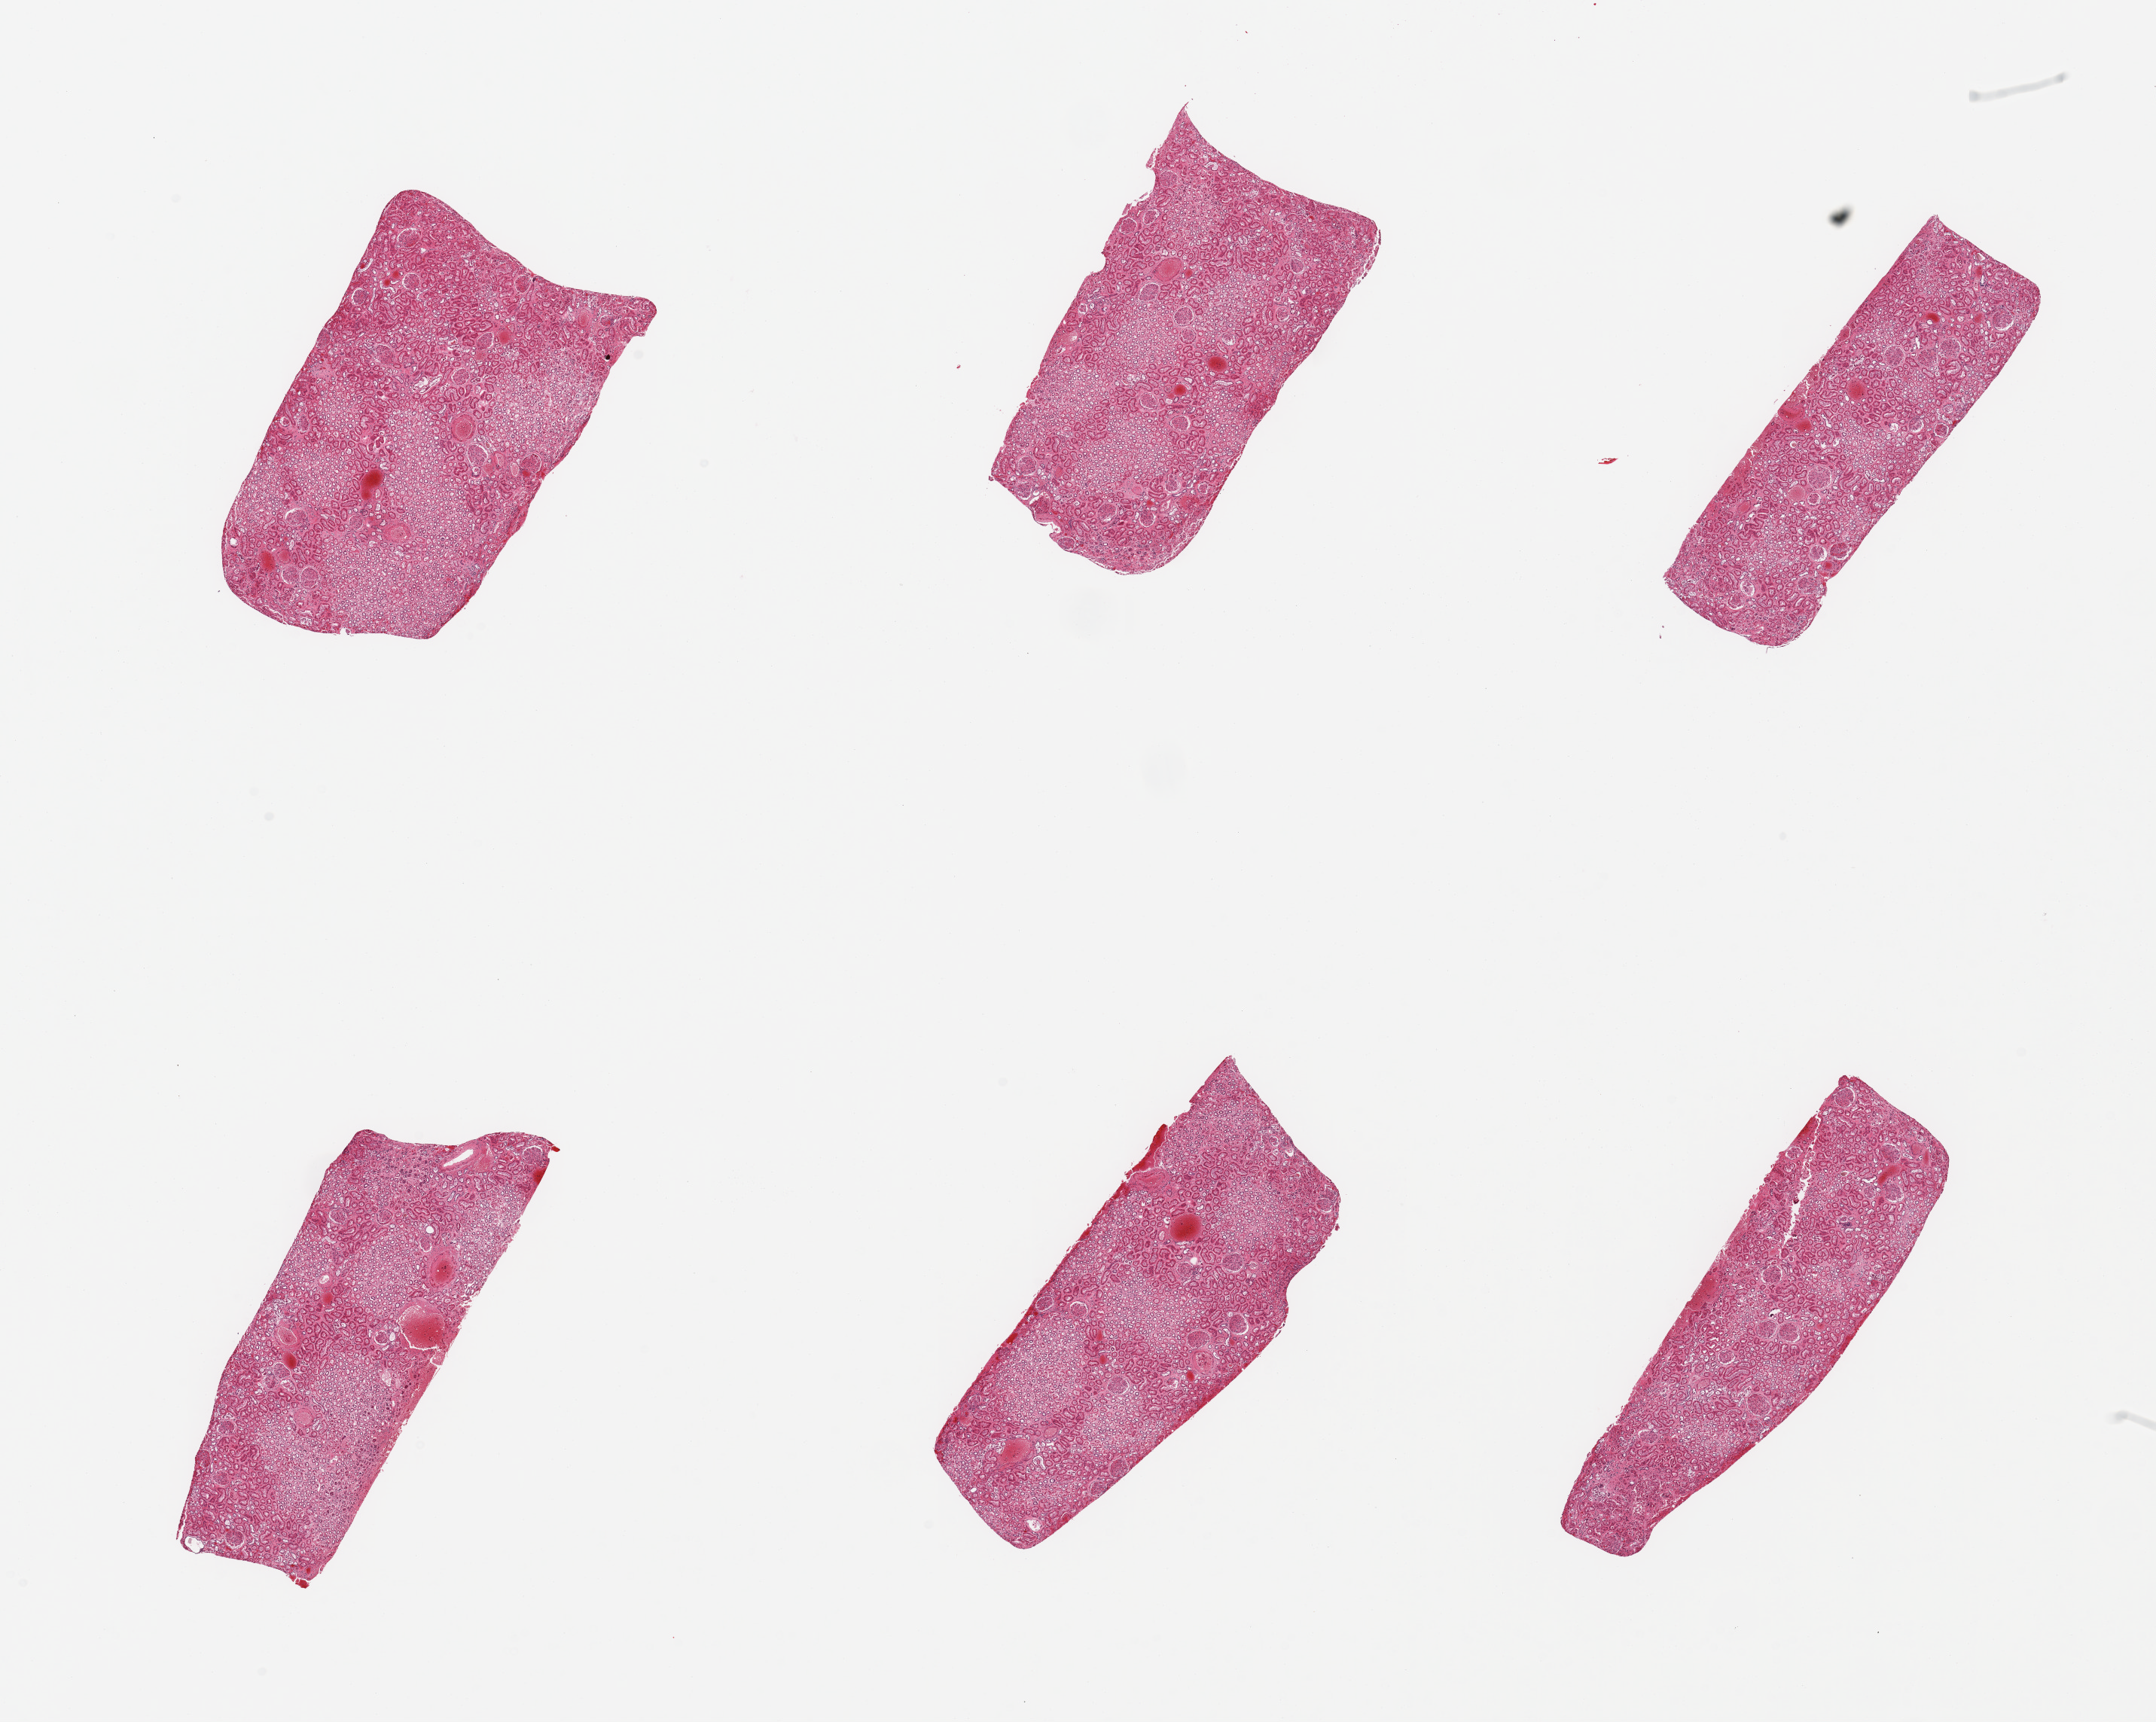
Hematoxylin and eosin (H&E) whole-slide image — low-resolution overview of the scanned area, about 22.6 x 18.1 mm; PAXgene-fixed, paraffin-embedded tissue; target tissue: renal cortex; donor tissue sample. Donor: female.
Pathologist's review note for this sample: 6 pieces; congested, arterio/arteriolosclerosis, rare sclerotic glomerulus.